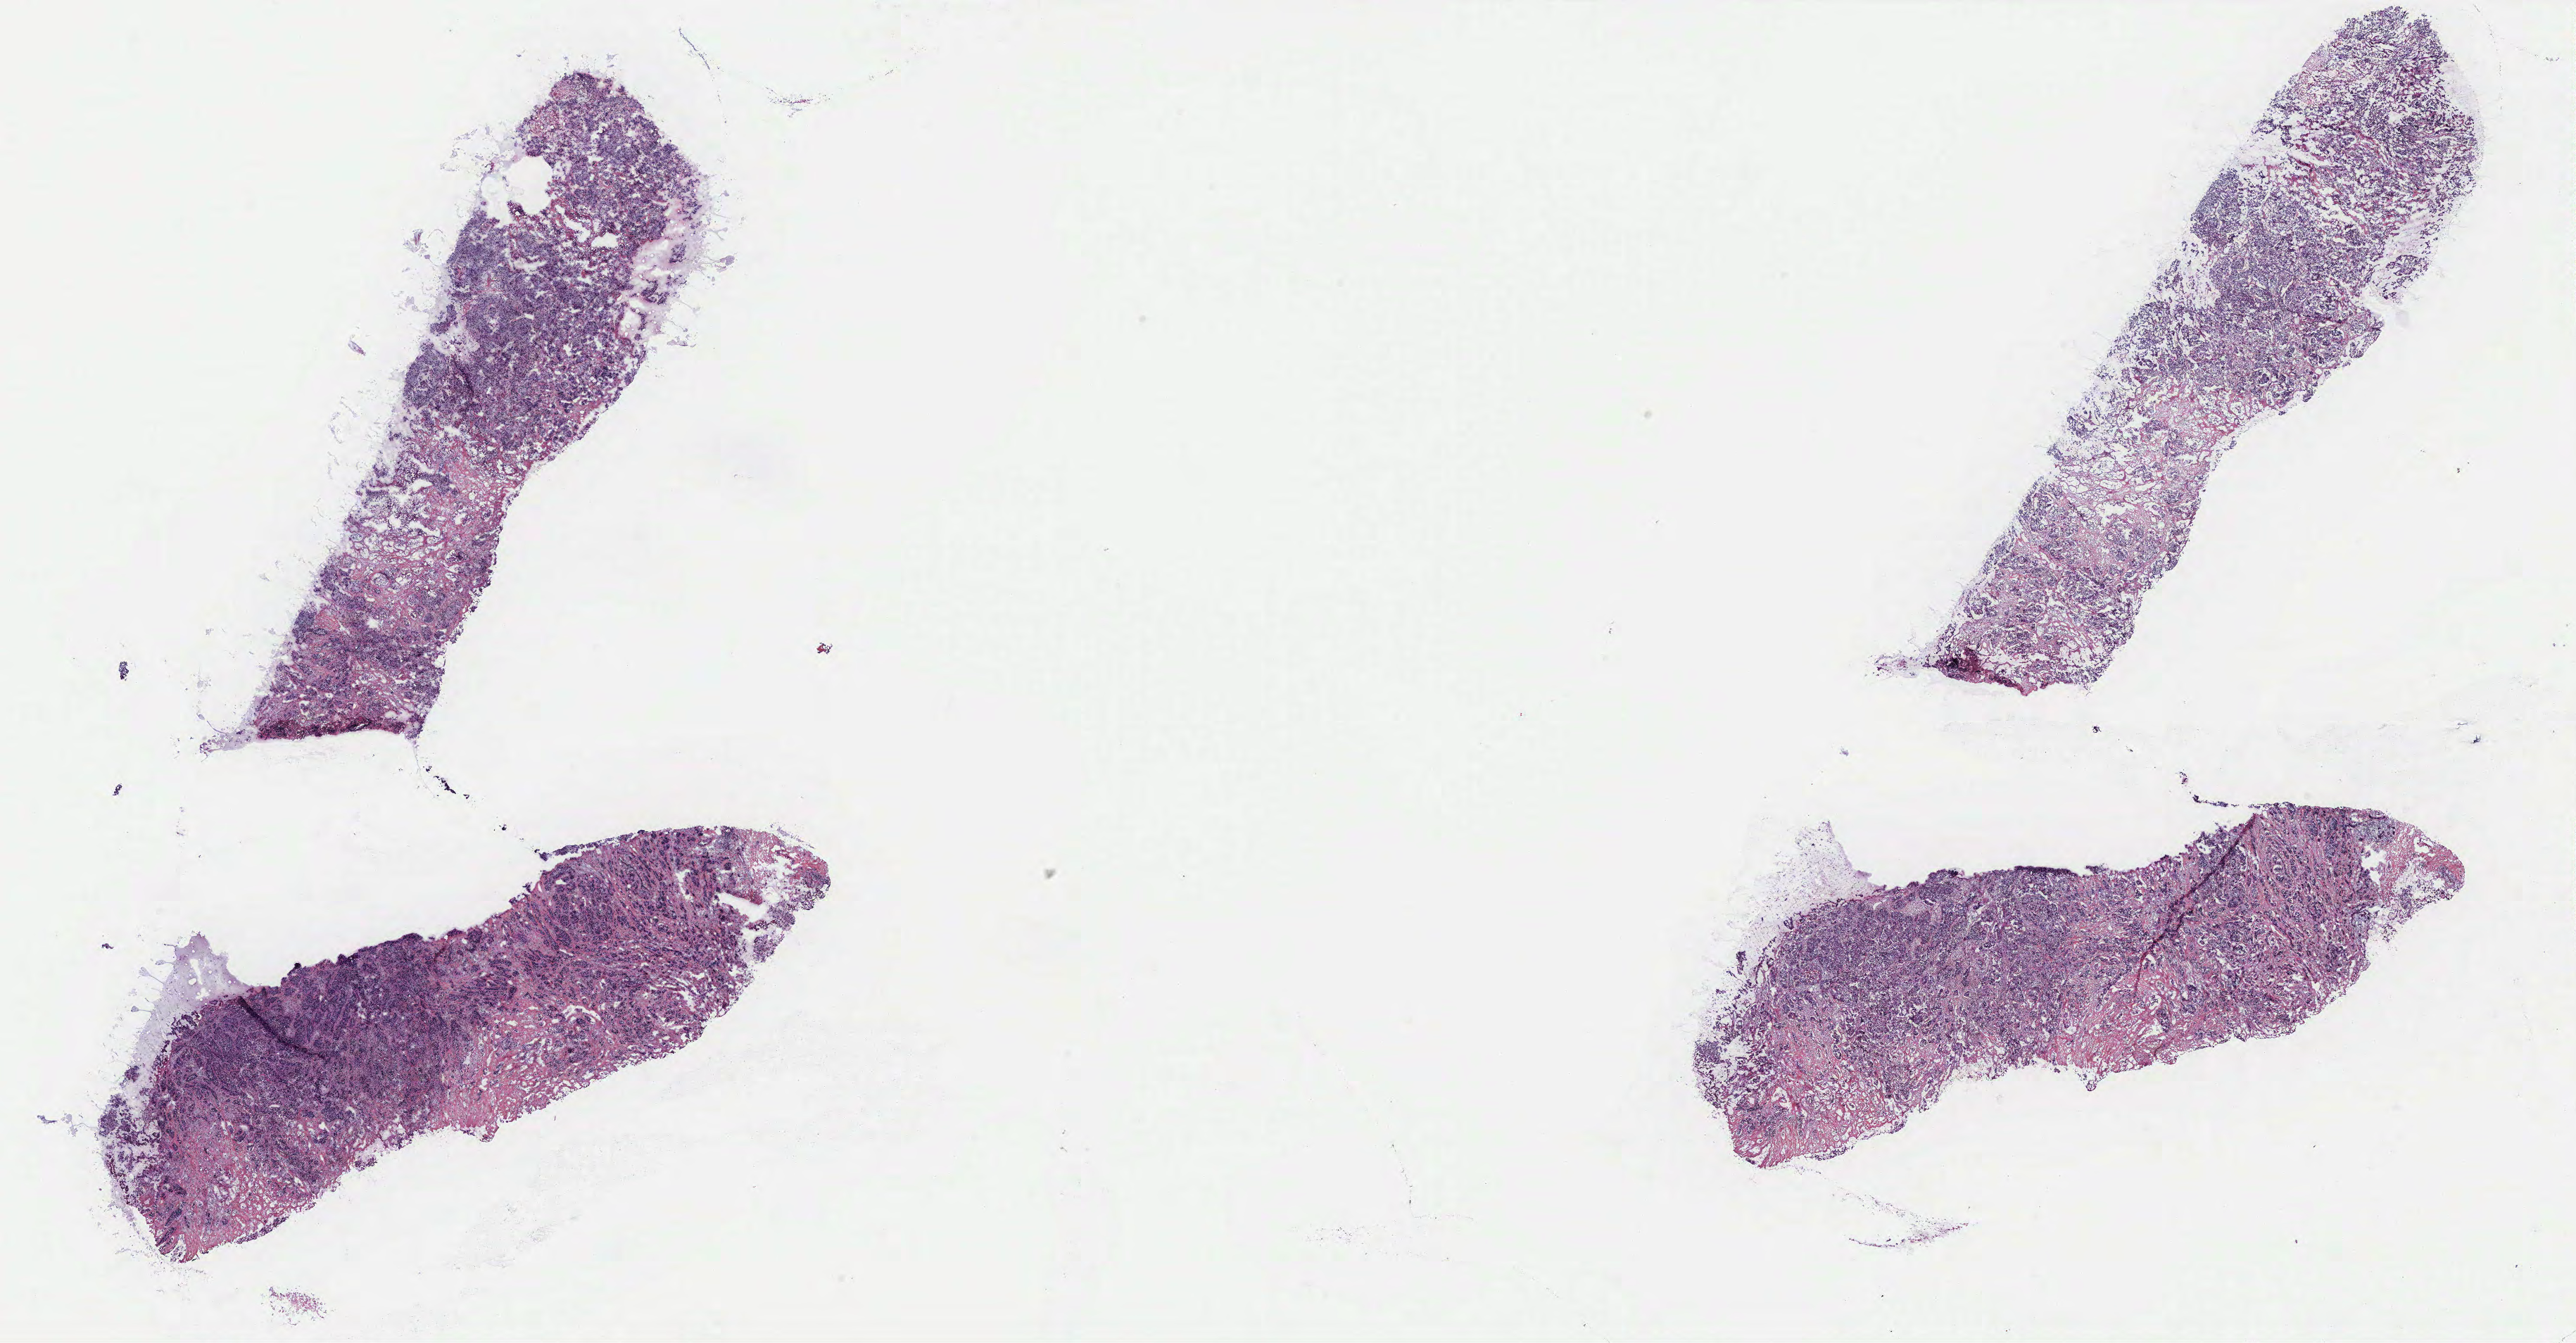
Whole-slide histology image, H&E-stained — shown as a low-resolution overview of the whole scanned area (about 29.3 x 15.3 mm, from a 40x scan). Breast, tissue type not recorded. 54-year-old female patient.
Patient diagnosis: Infiltrating duct carcinoma, NOS.